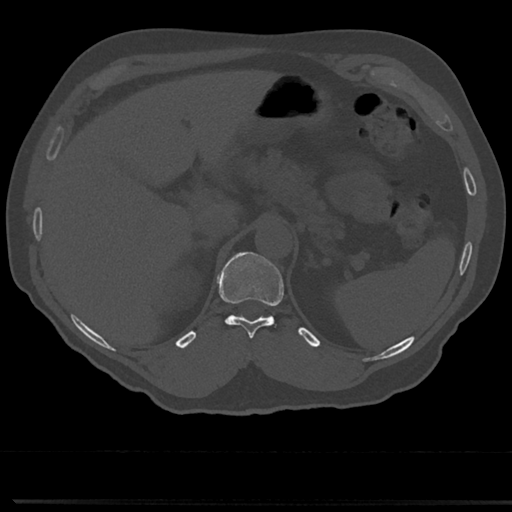
CT including the spine, one axial slice; position 195 of 817 along the scan axis; 120 kVp; bone window (W 1800 / L 400 HU); 0.5 mm slice thickness; 512 × 512 image matrix. Male patient, age 61 years. Case-level facts recorded for this patient, not image findings: primary cancer: prostate.
Structures marked on this image (semi-automatic segmentation, software-assisted and operator-edited):
- T11 vertebra: bounding box <220,255,284,340> (left, top, right, bottom; pixels)
- T12 vertebra: <222,253,250,279>